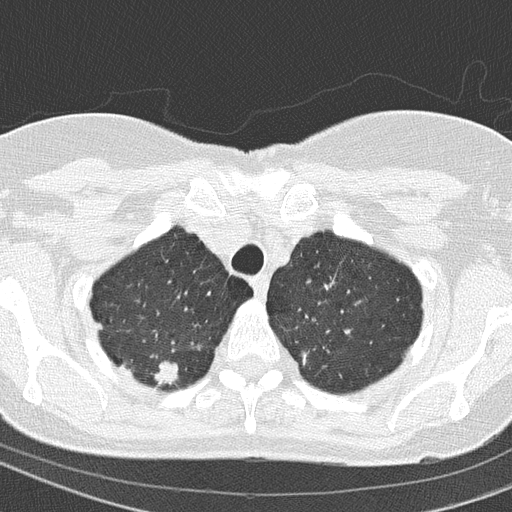
Chest CT (low-dose screening protocol), one axial image, baseline annual screen, lung window (W 1500 / L -600 HU), lung (sharp) reconstruction kernel (B50f), 120 kVp, slice 23 of 154 in the series. Female, age 67 years at enrolment. Current smoker at enrolment.
Expert-annotated lung lesion, bounding box [x1, y1, x2, y2] px = [130, 344, 191, 394]. The exam's reader record, not a measurement of the box and not confirmed to be the same lesion: non-calcified nodule or mass ≥4 mm, right upper lobe, 15 × 14 mm, spiculated (stellate) margins, soft tissue attenuation. Official screen result: positive, change unspecified: nodule(s) >= 4 mm or enlarging nodule(s), mass(es), or other non-specific abnormalities suspicious for lung cancer.